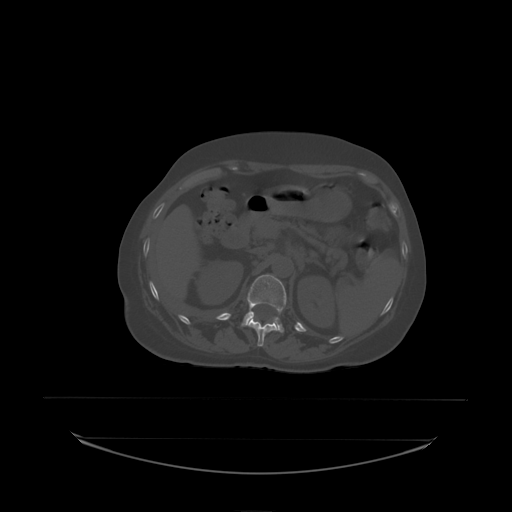
CT including the spine, one axial slice. Position 88 of 242 along the scan axis. Bone window (W 1800 / L 400 HU). 2.5 mm slice thickness. 512 × 512 image matrix, field of view 500 × 500 mm. Patient: female, 53 years. From the clinical record (not read from this slice): primary cancer: lung; vertebrae with lytic lesions (as recorded): T7, L1.
Outlined on this slice (semi-automatically segmented with operator editing):
- L1 vertebra: box from (x=241, y=275) to (x=287, y=333) px
- T12 vertebra: (x=248, y=318)–(x=278, y=338)